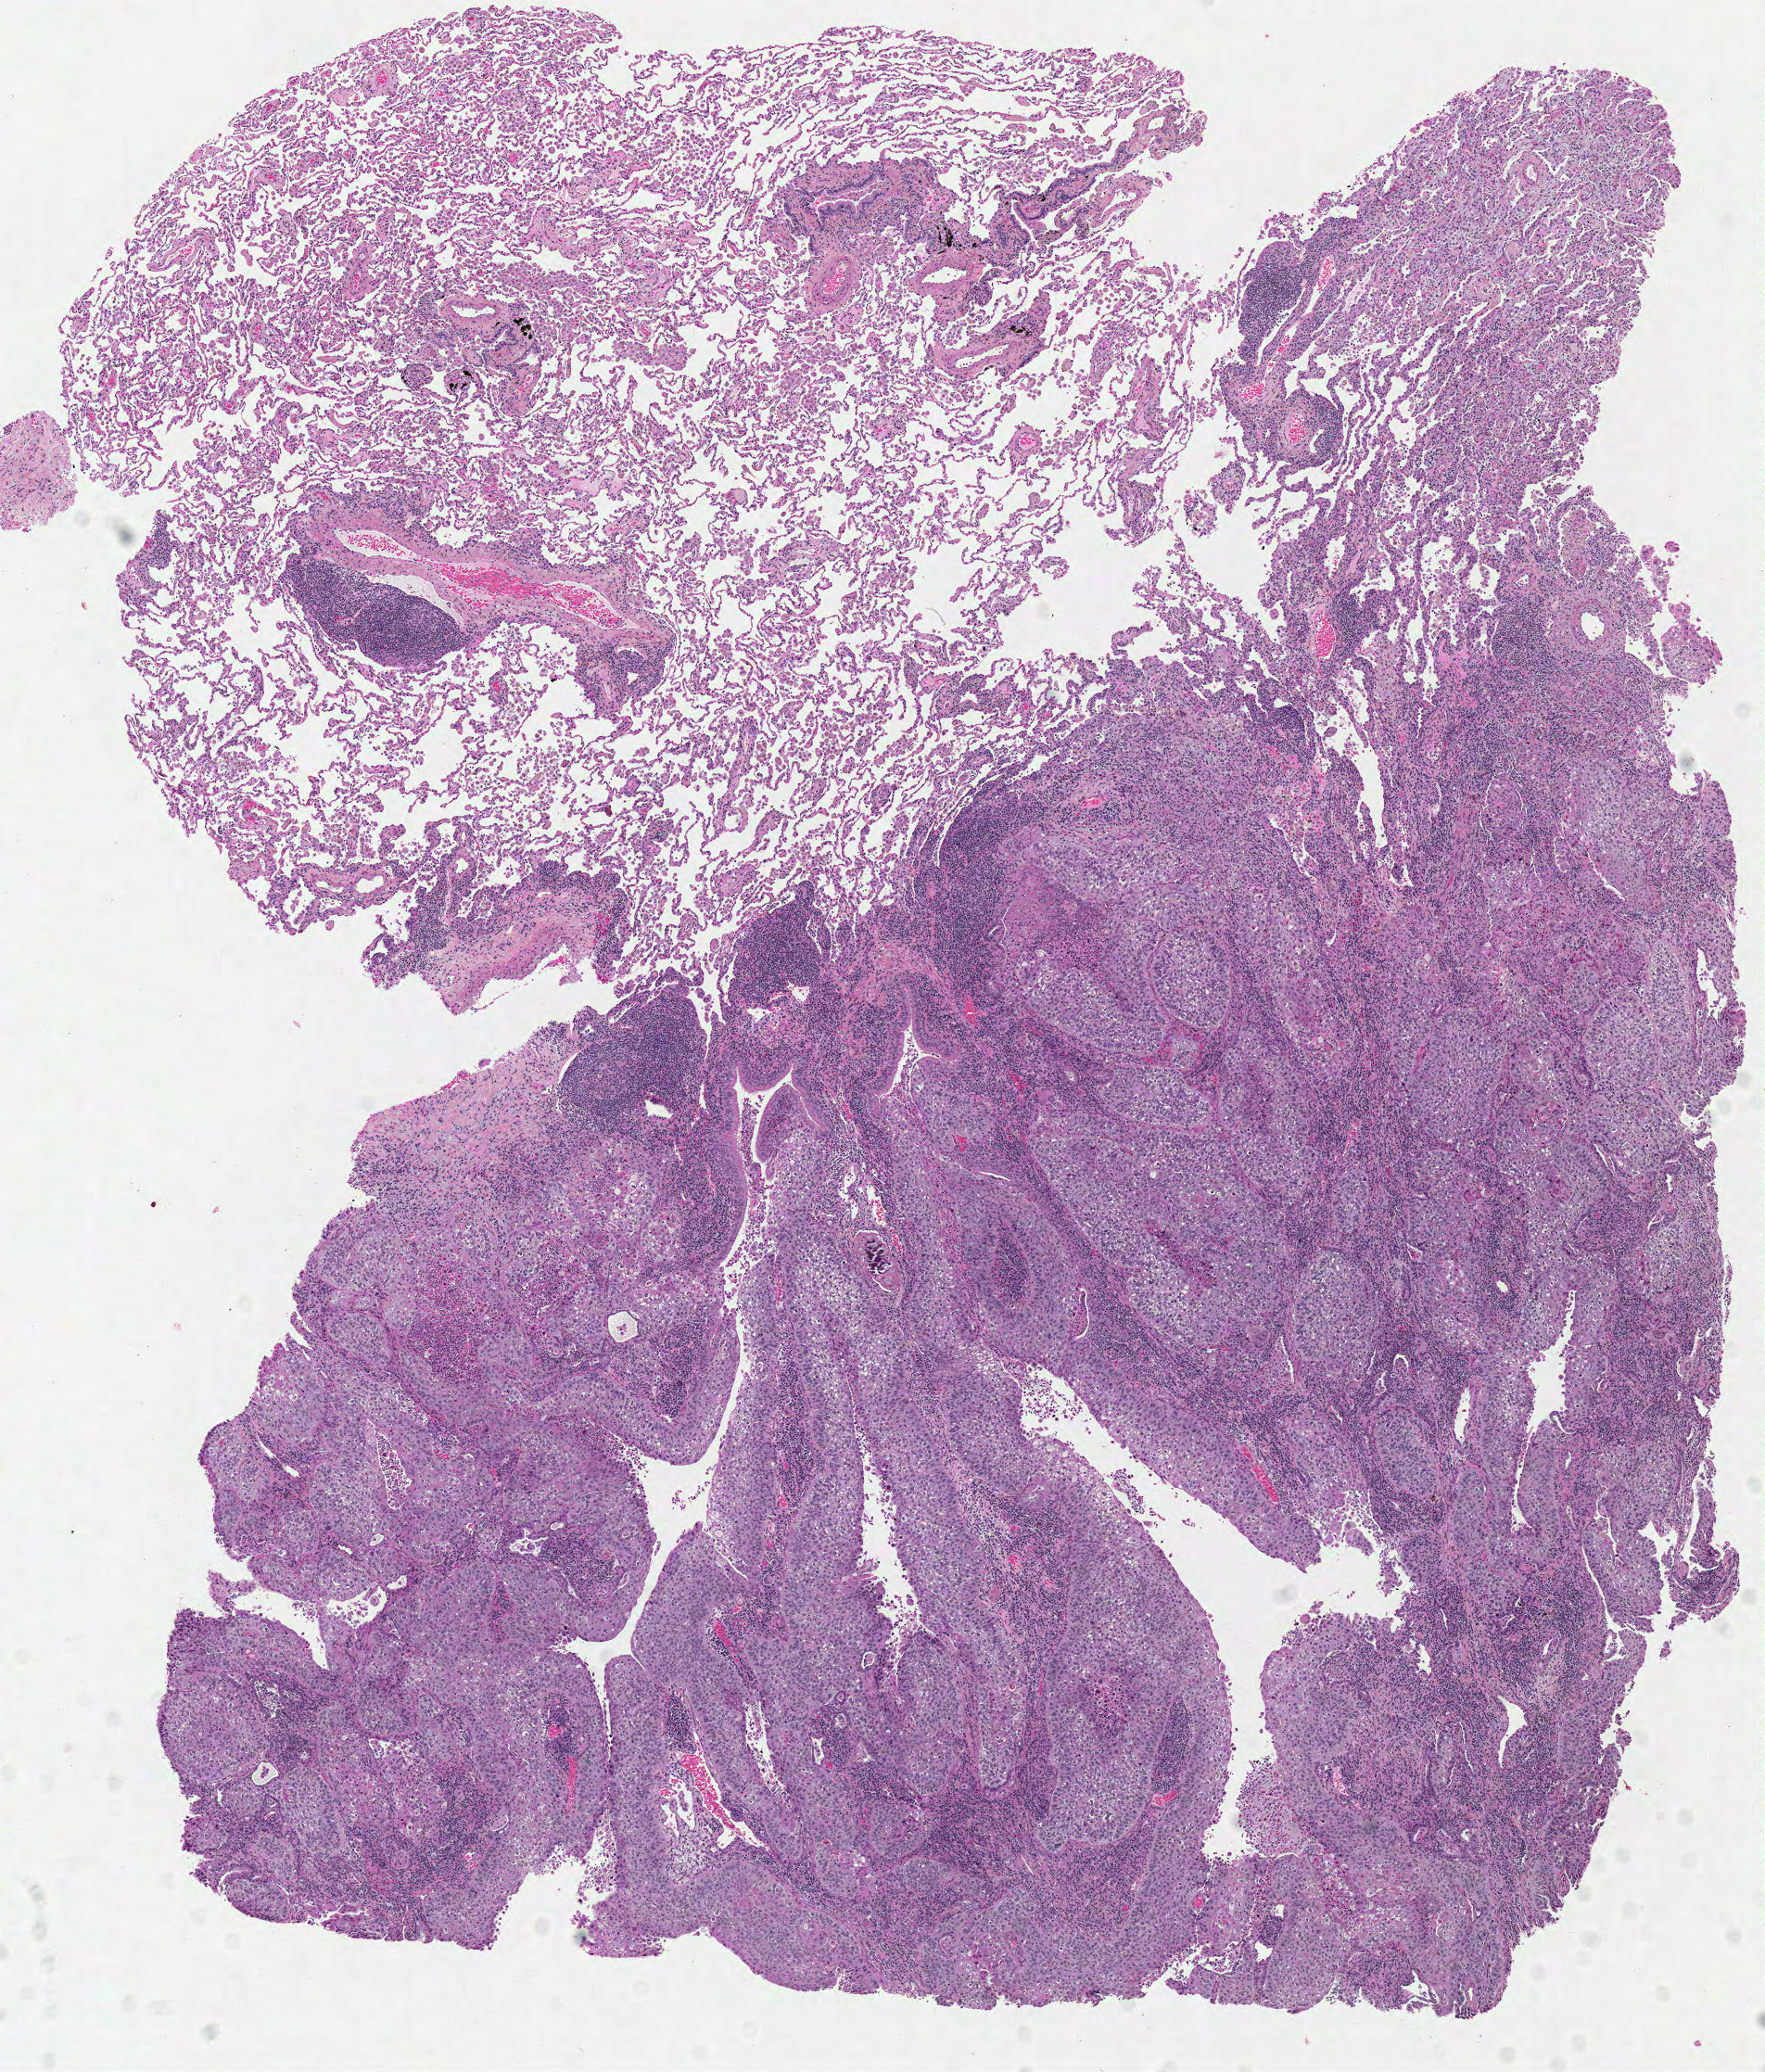
Whole-slide histology image, Hematoxylin and eosin (H&E) stained — a low-resolution overview of the entire scanned area, about 7.5 x 8.8 mm (acquisition: 40x scan), formalin-fixed paraffin-embedded (FFPE) diagnostic section, sample: primary tumour, lung. Male patient; age at initial diagnosis 56 years.
- AJCC pathologic stage: IB
- pathologic diagnosis: Squamous cell carcinoma, NOS (lower lobe, lung)